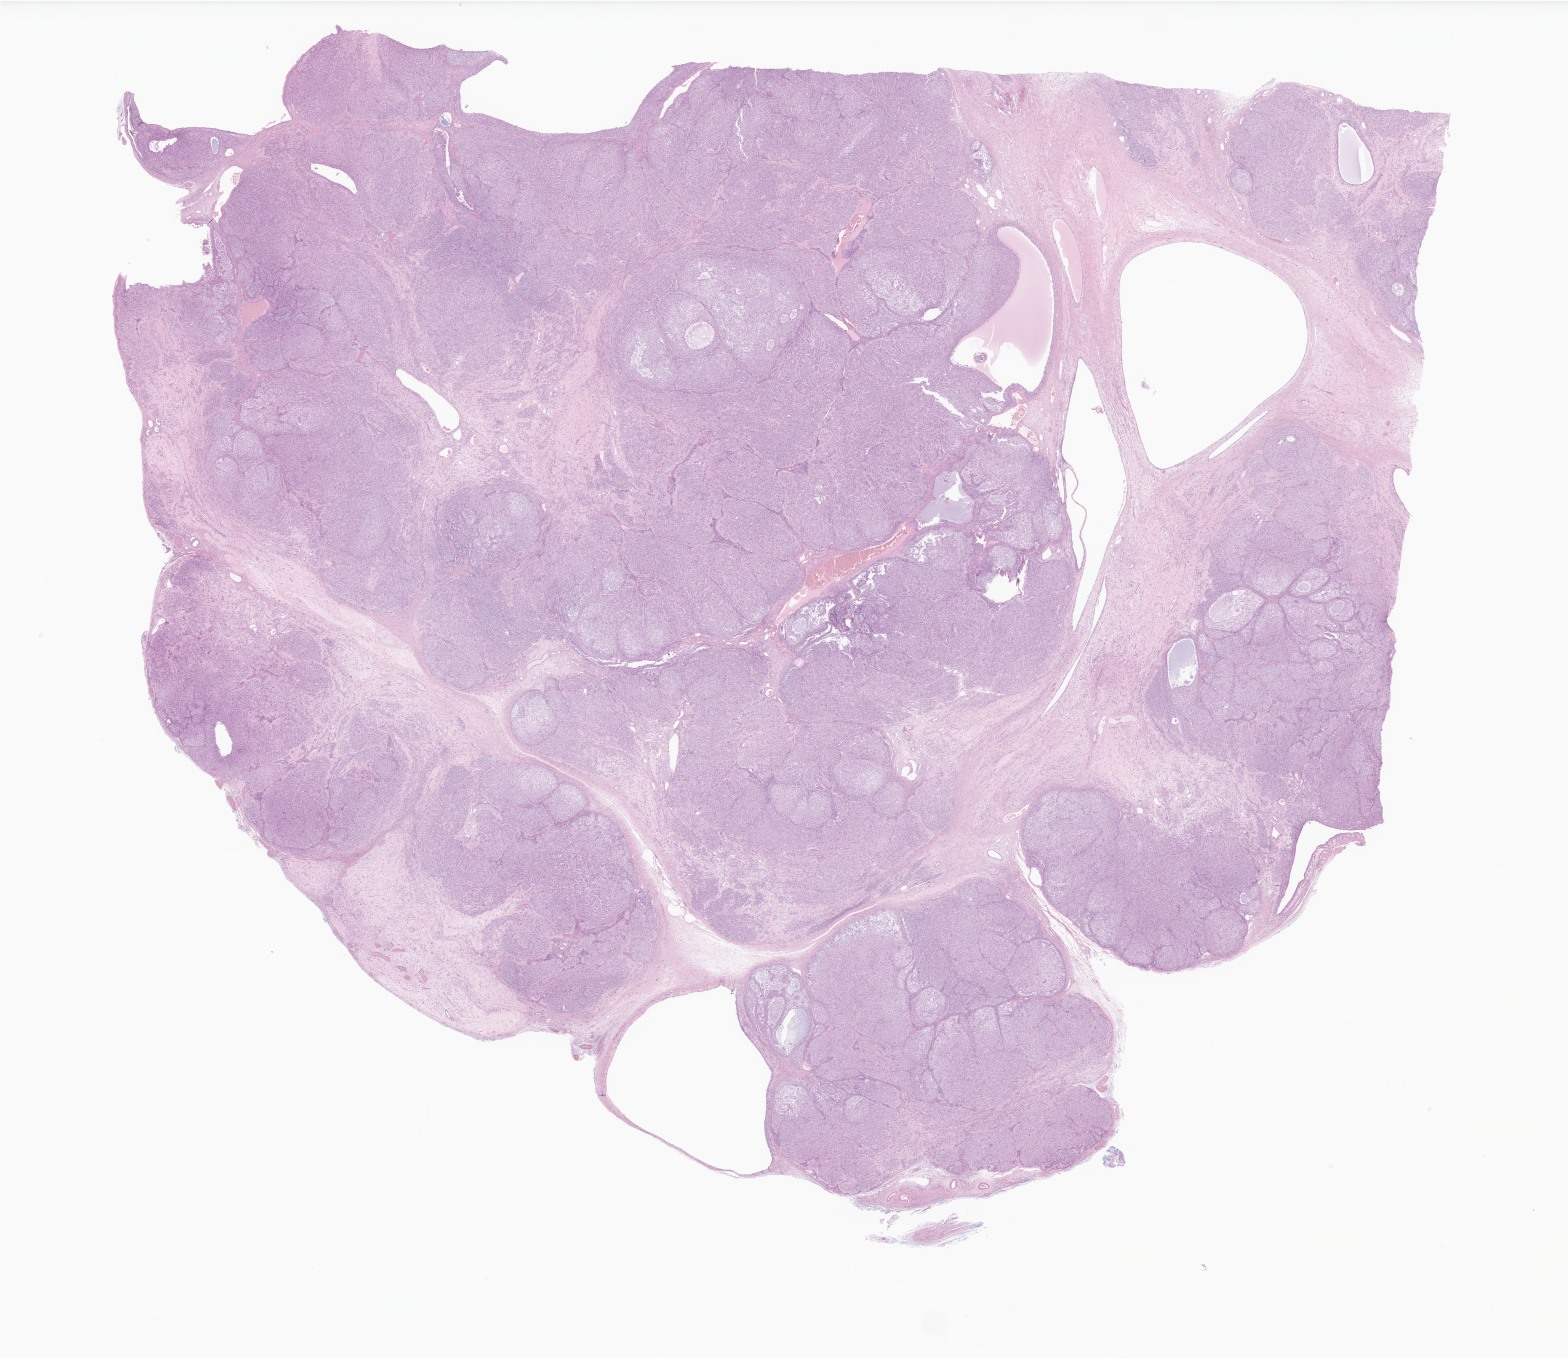
Digitized H&E-stained section of tumor tissue from the ovary, shown as a low-resolution overview of the whole scanned area (about 26.4 x 22.9 mm), FFPE section. Patient female; age 76 months.
• recorded diagnosis: Sex cord-gonadal stromal tumor, NOS